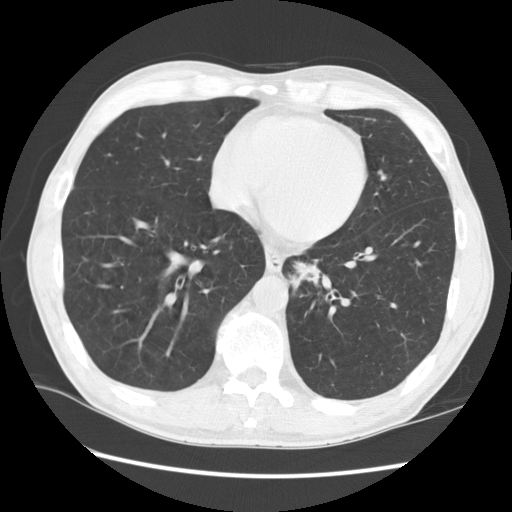
Chest CT (low-dose screening protocol), one axial image. Baseline screening round. Lung window (W 1500 / L -600 HU). 2.5 mm slice thickness. Standard (soft-tissue) reconstruction kernel (STANDARD). 120 kVp. Slice 96 of 141 in the series. Male, age 57 years at enrolment. Current smoker at enrolment.
Lesion marked by an expert reader, bounding box <268,246,342,310> (left, top, right, bottom; pixels). The screening reader recorded 2 non-calcified nodules or masses ≥4 mm on this exam (left lower lobe, lingula); which of them this box marks is not recorded. Official screen result: positive, change unspecified: nodule(s) >= 4 mm or enlarging nodule(s), mass(es), or other non-specific abnormalities suspicious for lung cancer. Participant outcome: lung cancer diagnosed 95 days after this screen — squamous cell carcinoma, NOS, left lower lobe, moderately differentiated (G2), stage IB (AJCC 6th edition), 35 mm at pathology.